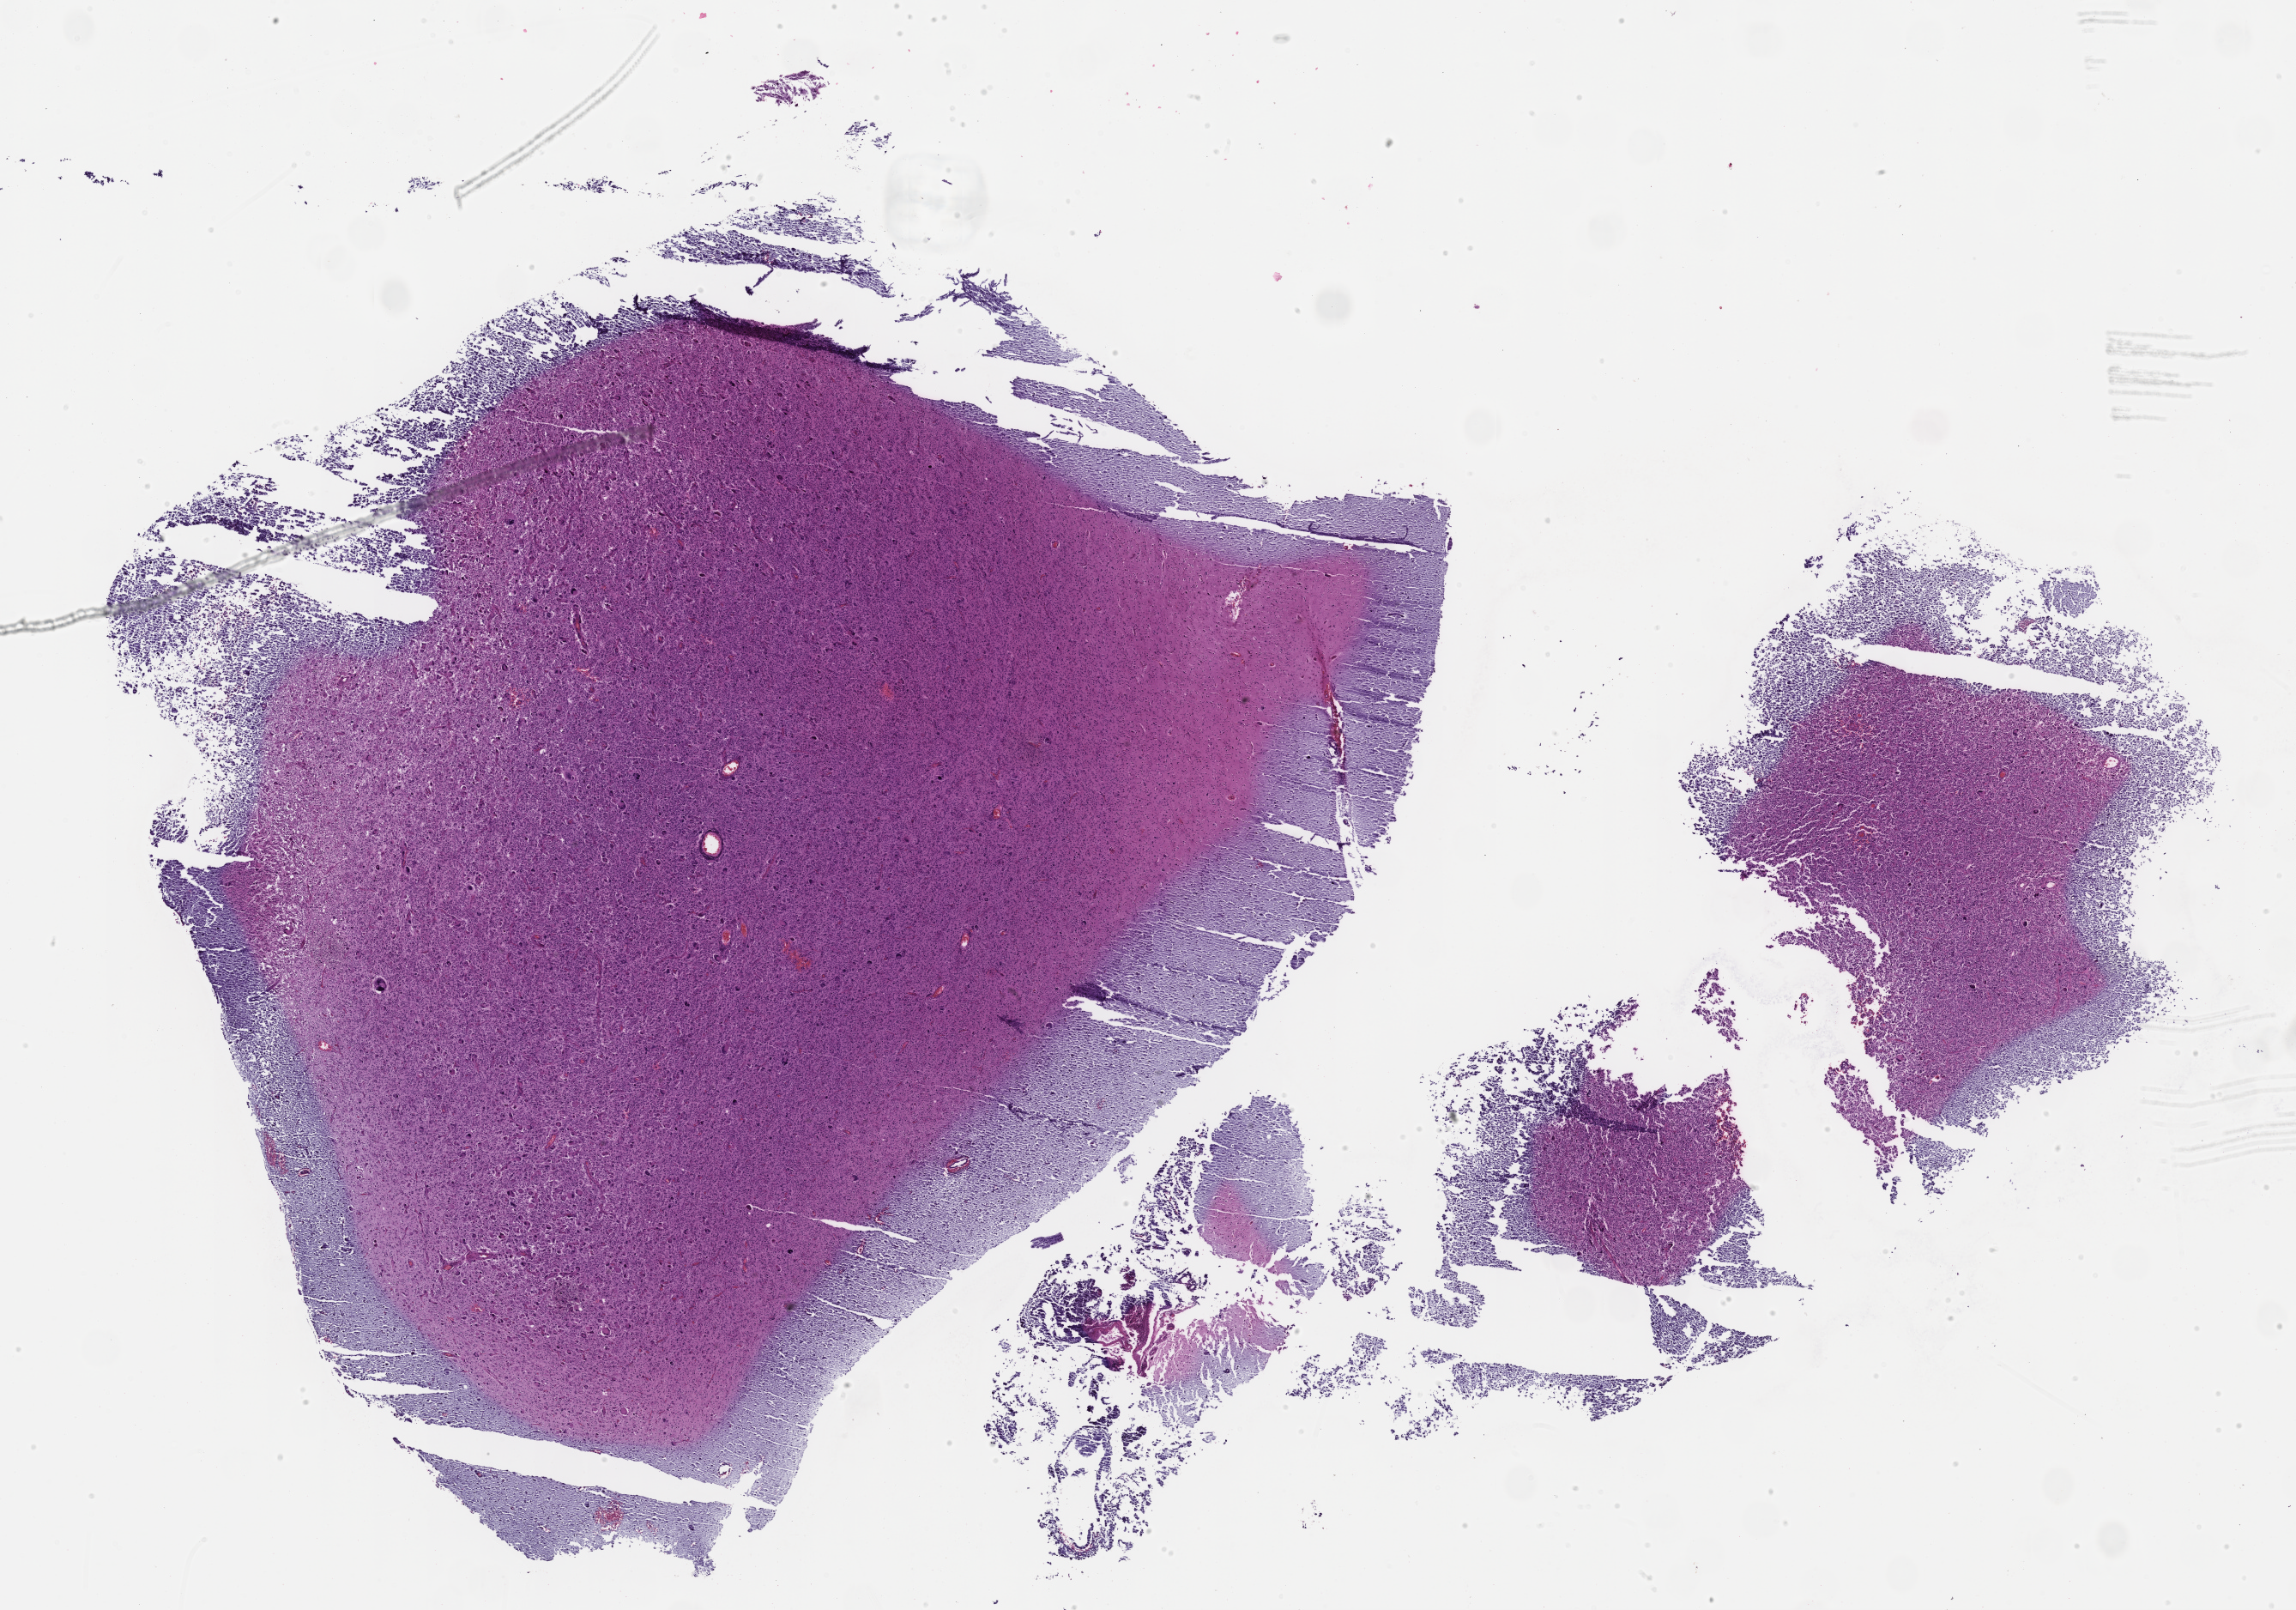
Hematoxylin and eosin (H&E) stained whole-slide image, shown as a low-resolution overview of the whole scanned area (about 21.7 x 15.2 mm, from a 40x scan), FFPE section, primary tumour sample from the brain. Patient: male, age at initial diagnosis 41 years.
- diagnosis: Glioblastoma